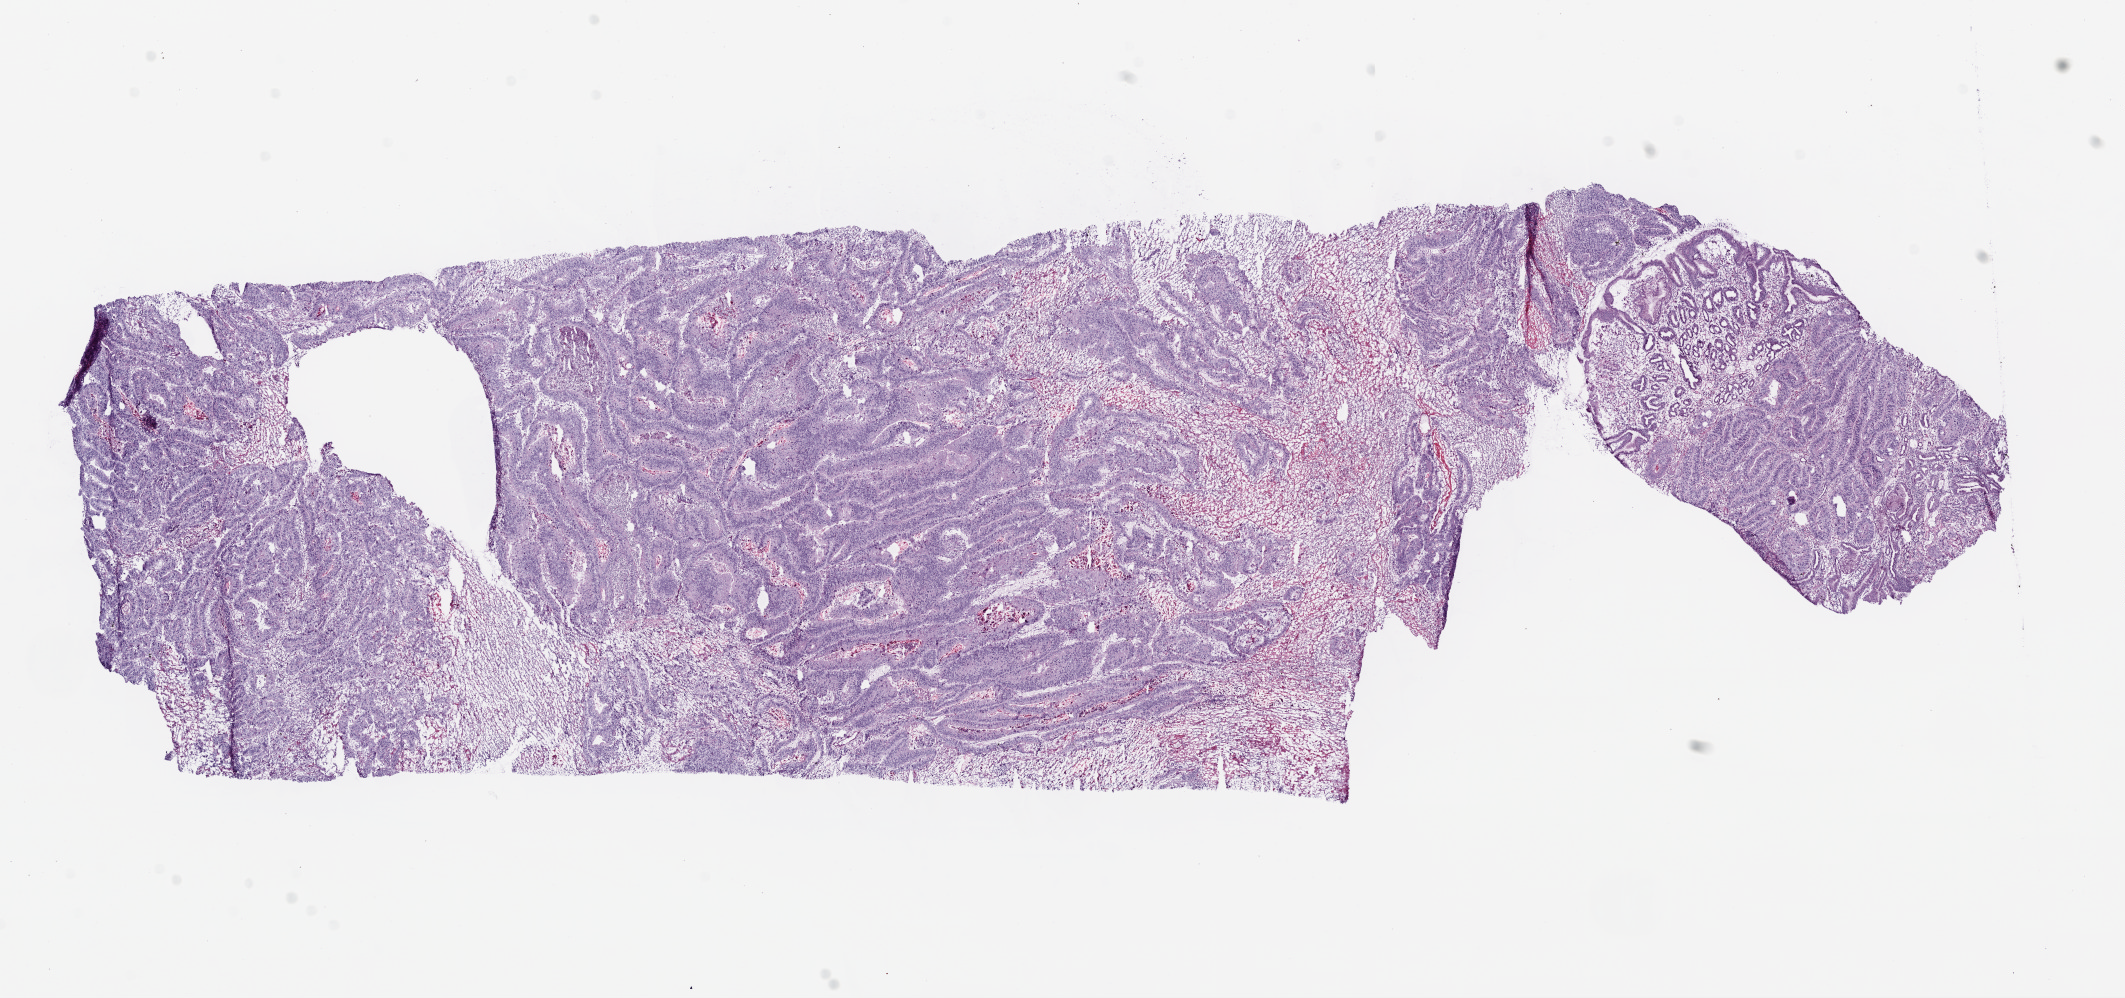
Digitized H&E-stained tissue section (whole slide), shown as a low-resolution overview of the whole scanned area (about 17.1 x 8.0 mm, from a 20x scan); frozen section from the top of the tissue portion; stomach, primary tumour sample. Patient: male, age at initial diagnosis 57 years. Histologic grade: G2 (moderately differentiated). Slide review estimates, as recorded: tumour cells 65%, tumour nuclei 80%, normal cells 10%, stromal cells 20%, necrosis 5%.
Diagnosis: Adenocarcinoma, intestinal type. TNM: T2 N0 M0. AJCC pathologic stage: IB (6th edition).